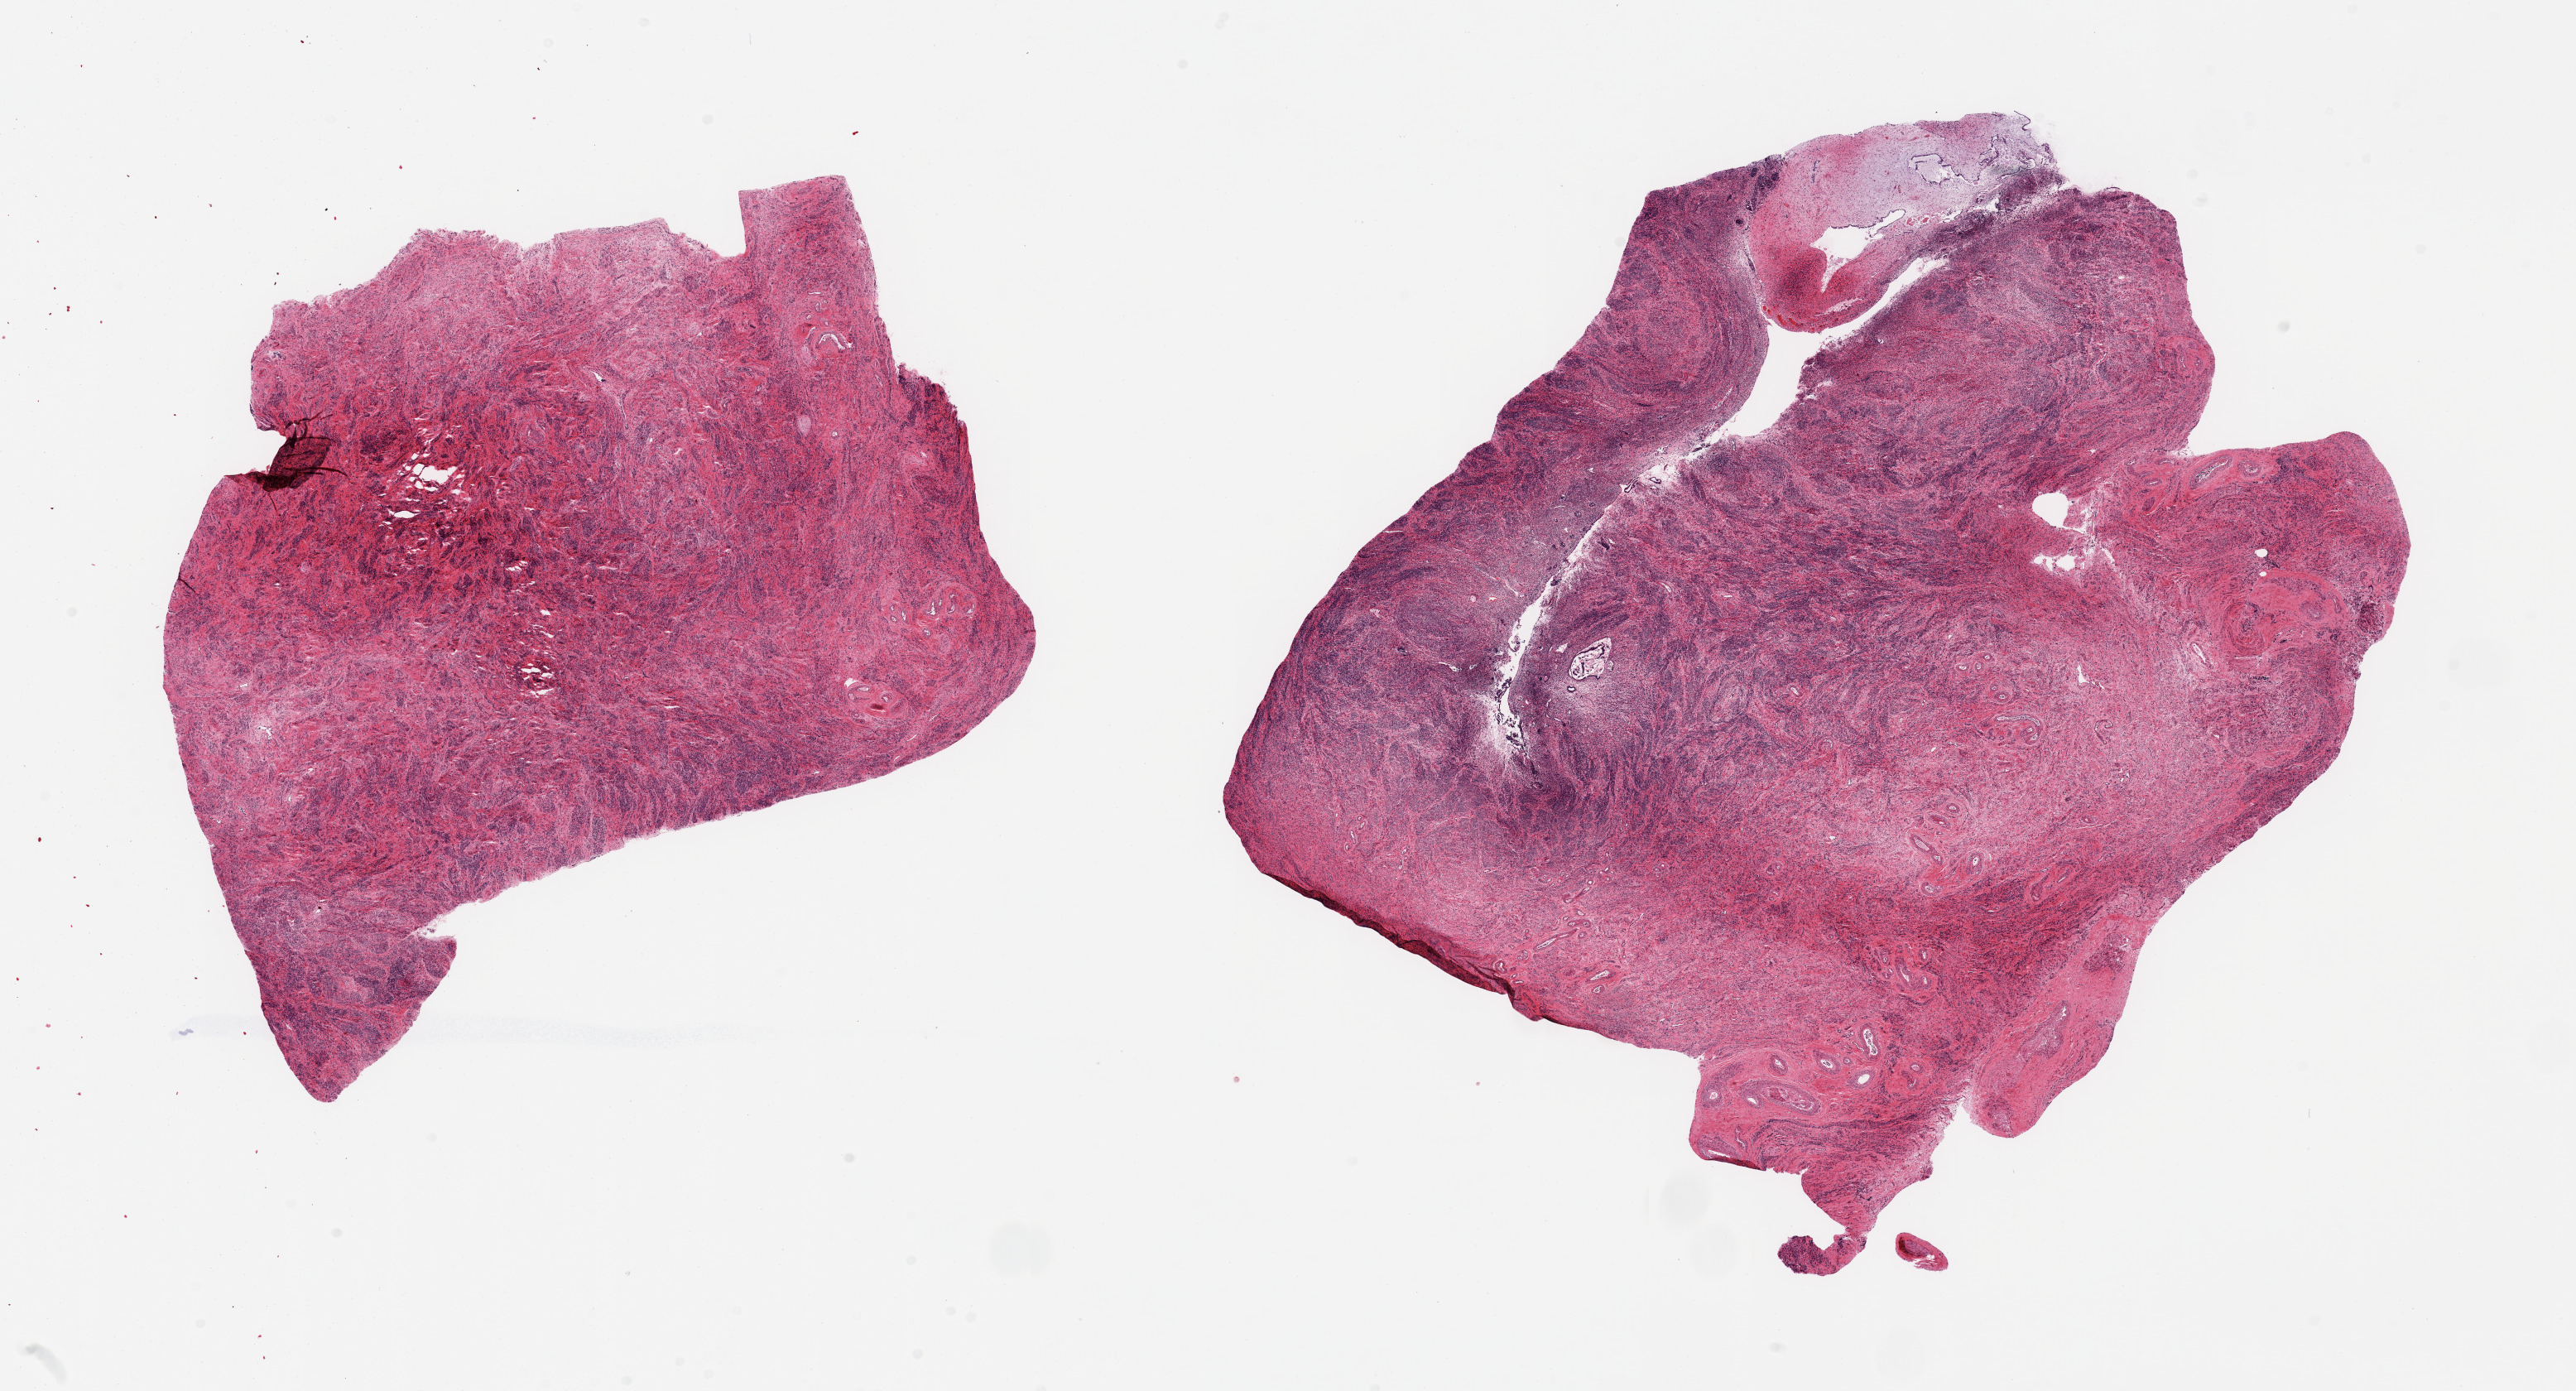
Whole-slide image, hematoxylin and eosin (H&E) stain, whole scanned area (about 24.6 x 13.3 mm) shown as a low-resolution overview; PAXgene-fixed paraffin-embedded (PFPE) section; target tissue: uterus; tissue donor sample. Female donor.
Pathologist's review note for this sample: 2 pieces, mainly myometrium, trace degenerated basalis endometrium noted (inactive).